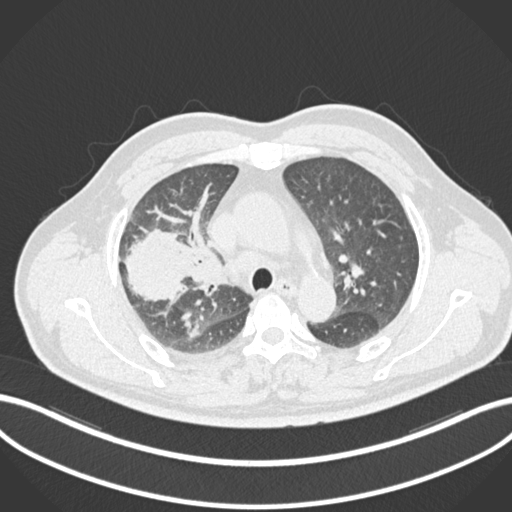
Chest CT, one axial slice; position 660 of 852 along the scan axis; reconstruction kernel B30f; lung window (W 1500 / L -600 HU); 512 × 512 image matrix, field of view 400 × 400 mm. Patient: male, 55 years. Case-level facts recorded for this patient, not image findings: clinical TNM (as recorded): T3 N2 M1.
Structures marked on this image (bounding box drawn by a radiologist):
- lung tumour (recorded histology: adenocarcinoma): box from (x=119, y=229) to (x=199, y=305) px